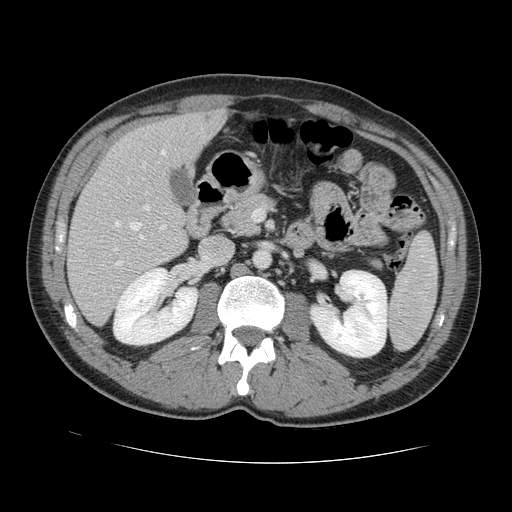
Contrast-enhanced abdominal CT, one axial slice. Position 64 of 131 along the scan axis. 120 kVp. Intravenous contrast given. Soft-tissue window (W 400 / L 40 HU). 2.5 mm slice thickness. 512 × 512 image matrix. Male patient, age 40 years. From the clinical record (not read from this slice): diagnosis: colorectal cancer liver metastases, imaged before liver resection; multiple liver metastases: yes; largest metastasis: 2.9 cm; disease in both lobes: yes.
Annotated regions visible in this slice (manually delineated by an expert):
- hepatic veins: bounding box [x1, y1, x2, y2] px = [114, 146, 166, 251]
- liver: [68, 112, 223, 324]
- planned liver remnant (the part of the liver to remain after resection): [109, 112, 223, 182]
- portal vein (with intrahepatic branches): [115, 205, 166, 266]
- liver metastasis: [205, 116, 212, 122]